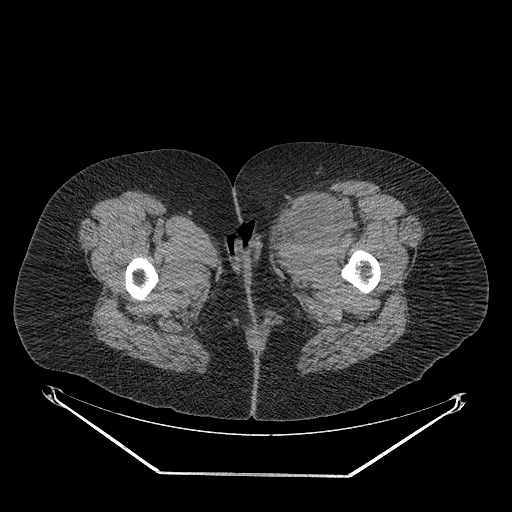
CT of an extremity soft-tissue mass (from a PET/CT study), one axial slice; position 39 of 267 along the scan axis; soft-tissue window (W 400 / L 40 HU); 3.75 mm slice thickness; 512 × 512 image matrix, field of view 500 × 500 mm. Female patient. From the clinical record (not read from this slice): histological type: myxofibrosarcoma; grade: intermediate; site of the primary tumour: left thigh.
Structures marked on this image (expert contour drawn on MRI and transferred to this co-registered scan by the dataset authors):
- gross tumour volume including surrounding oedema: bounding box <267,194,359,254> (left, top, right, bottom; pixels)
- gross tumour volume (mass): <274,194,346,243>